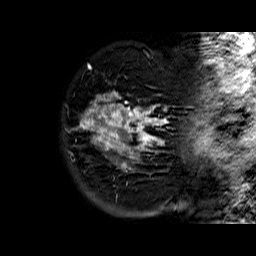
Breast MRI (dynamic contrast-enhanced), one sagittal slice; position 9 of 60 along the scan axis; dynamic contrast-enhanced series, time point 2 of 6 at this slice position (early post-contrast); 1.5 T; TE 6.3 ms, TR 32.4 ms; 256 × 256 image matrix. Female patient. From the clinical record (not read from this slice): setting: breast cancer imaged before/during neoadjuvant chemotherapy; receptor status: HR-positive, HER2-negative.
Outlined on this slice (semi-automatically segmented with operator editing):
- analysis volume of interest (the breast-tissue region the enhancement analysis was run in; not a lesion): box from (x=73, y=74) to (x=174, y=173) px
- tumour enhancement mask (voxels above the 100 % enhancement threshold inside the analysis volume of interest): (x=76, y=91)–(x=168, y=168)